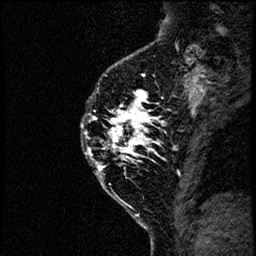
Breast MRI (dynamic contrast-enhanced), one sagittal slice; position 49 of 60 along the scan axis; dynamic contrast-enhanced study with each time point stored as its own series, time point 2 of 4 at this slice position (early post-contrast, ordered by acquisition time); 1.5 T; TE 4.2 ms, TR 17.6 ms; 256 × 256 image matrix. Patient: female, 40 years. Case-level facts recorded for this patient, not image findings: setting: breast cancer imaged before/during neoadjuvant chemotherapy; receptor status: HER2-positive.
Structures marked on this image (semi-automatically segmented with operator editing):
- analysis volume of interest (the breast-tissue region the enhancement analysis was run in; not a lesion): bounding box <76,55,185,206> (left, top, right, bottom; pixels)
- tumour enhancement mask (voxels above the 100 % enhancement threshold inside the analysis volume of interest): <81,92,181,178>